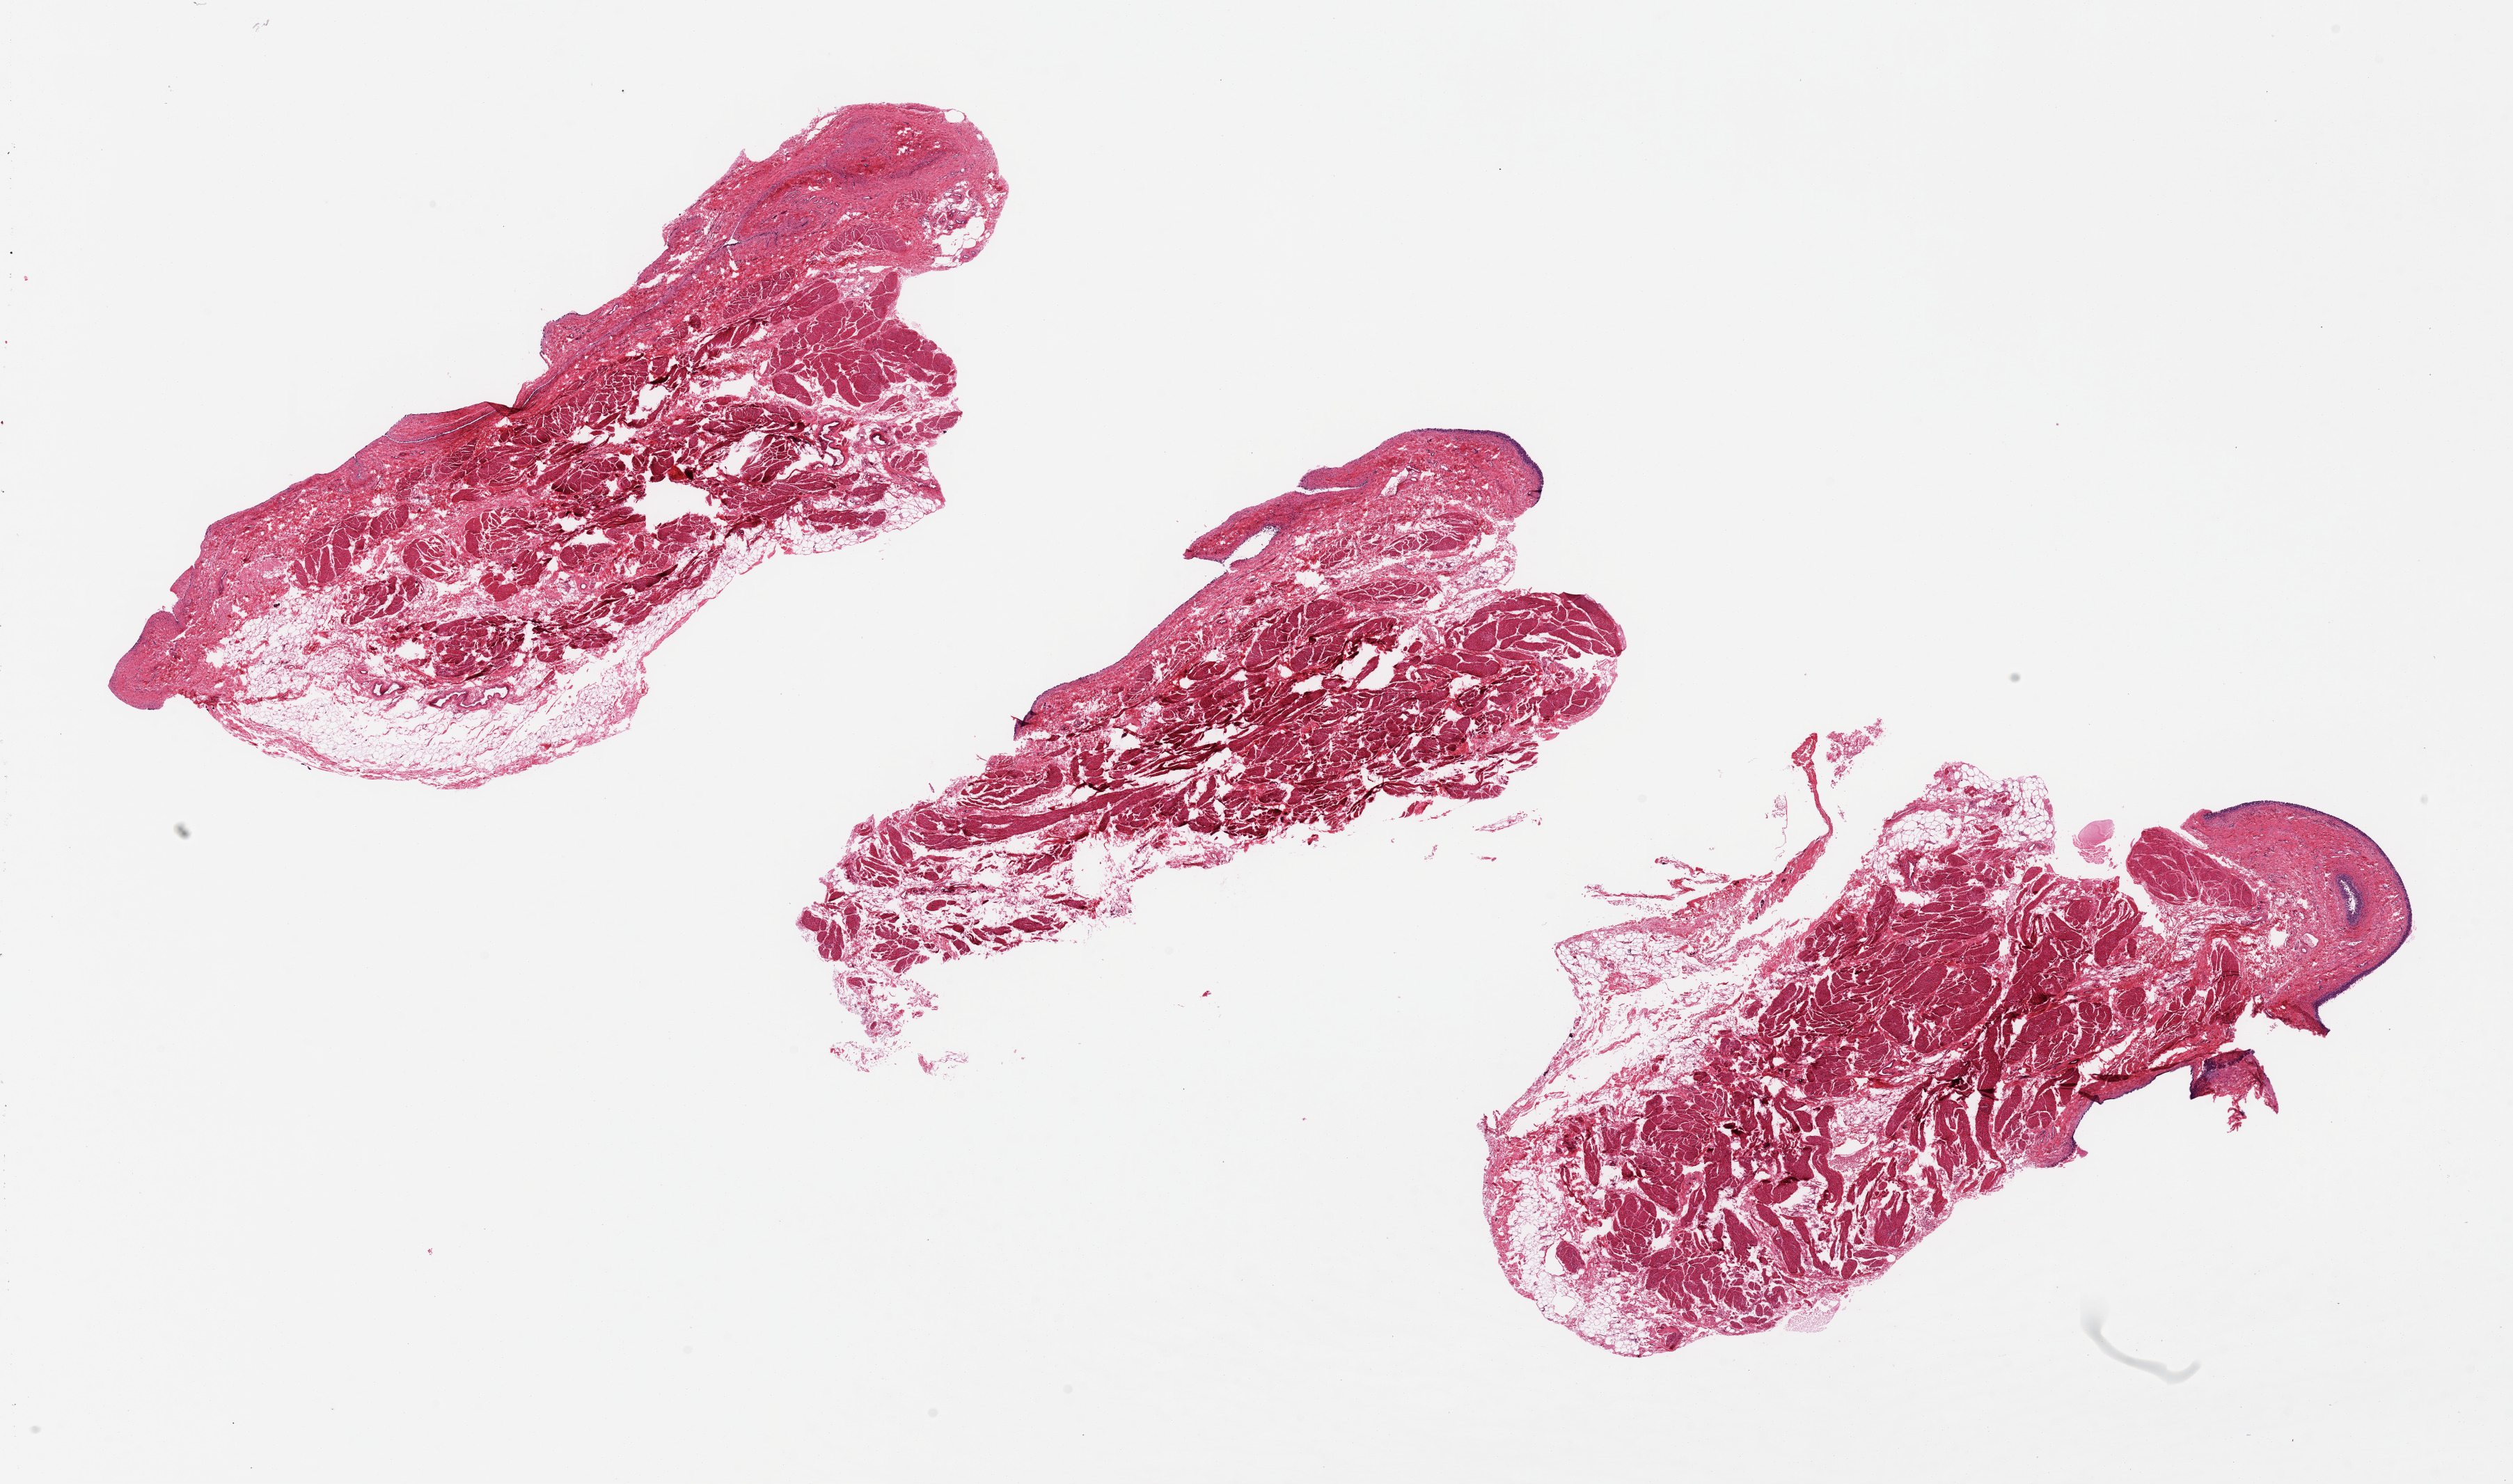
Whole-slide image, H&E stain, whole scanned area (about 28.5 x 16.9 mm) shown as a low-resolution overview, PAXgene-fixed, paraffin-embedded tissue, target tissue: urinary bladder, donor tissue sample. Donor sex: male.
* review note (as recorded): urothelium is 50-60% sloughed, less than 0.5% of specimen thickness